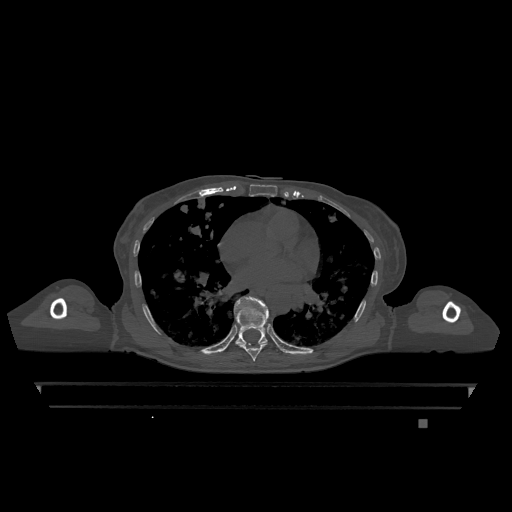
CT including the spine, one axial slice; position 716 of 1317 along the scan axis; bone window (W 1800 / L 400 HU); 0.5 mm slice thickness; 512 × 512 image matrix, field of view 500 × 500 mm. Female patient, age 74 years. From the clinical record (not read from this slice): primary cancer: lung; vertebrae with lytic lesions (as recorded): T1, T4, T5, T6, L4, L5.
Annotated regions visible in this slice (semi-automatic segmentation, software-assisted and operator-edited):
- T7 vertebra: bounding box <238,343,268,361> (left, top, right, bottom; pixels)
- T9 vertebra: <234,297,269,345>